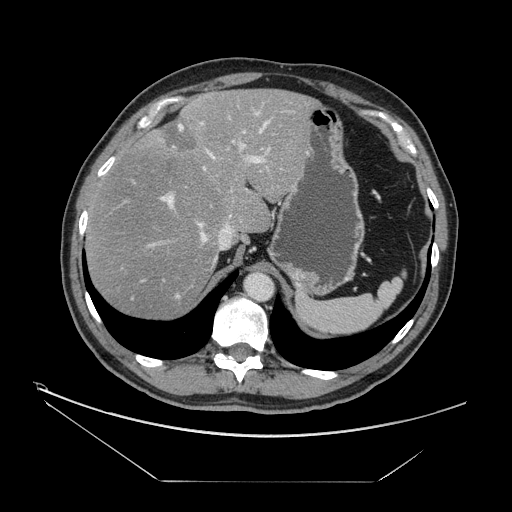
Contrast-enhanced abdominal CT, one axial slice. Slice 114 of 161 in the series (ordered by position). Intravenous contrast given. Soft-tissue window (W 400 / L 40 HU). 512 × 512 image matrix. Male patient, age 65 years. From the clinical record (not read from this slice): diagnosis: colorectal cancer liver metastases, imaged before liver resection; multiple liver metastases: yes; largest metastasis: 4.2 cm.
Structures marked on this image (manually delineated by an expert):
- hepatic veins: bounding box <149,123,267,263> (left, top, right, bottom; pixels)
- liver: <86,90,315,319>
- planned liver remnant (the part of the liver to remain after resection): <86,90,315,319>
- portal vein (with intrahepatic branches): <159,109,290,226>
- liver metastasis: <161,122,197,157>